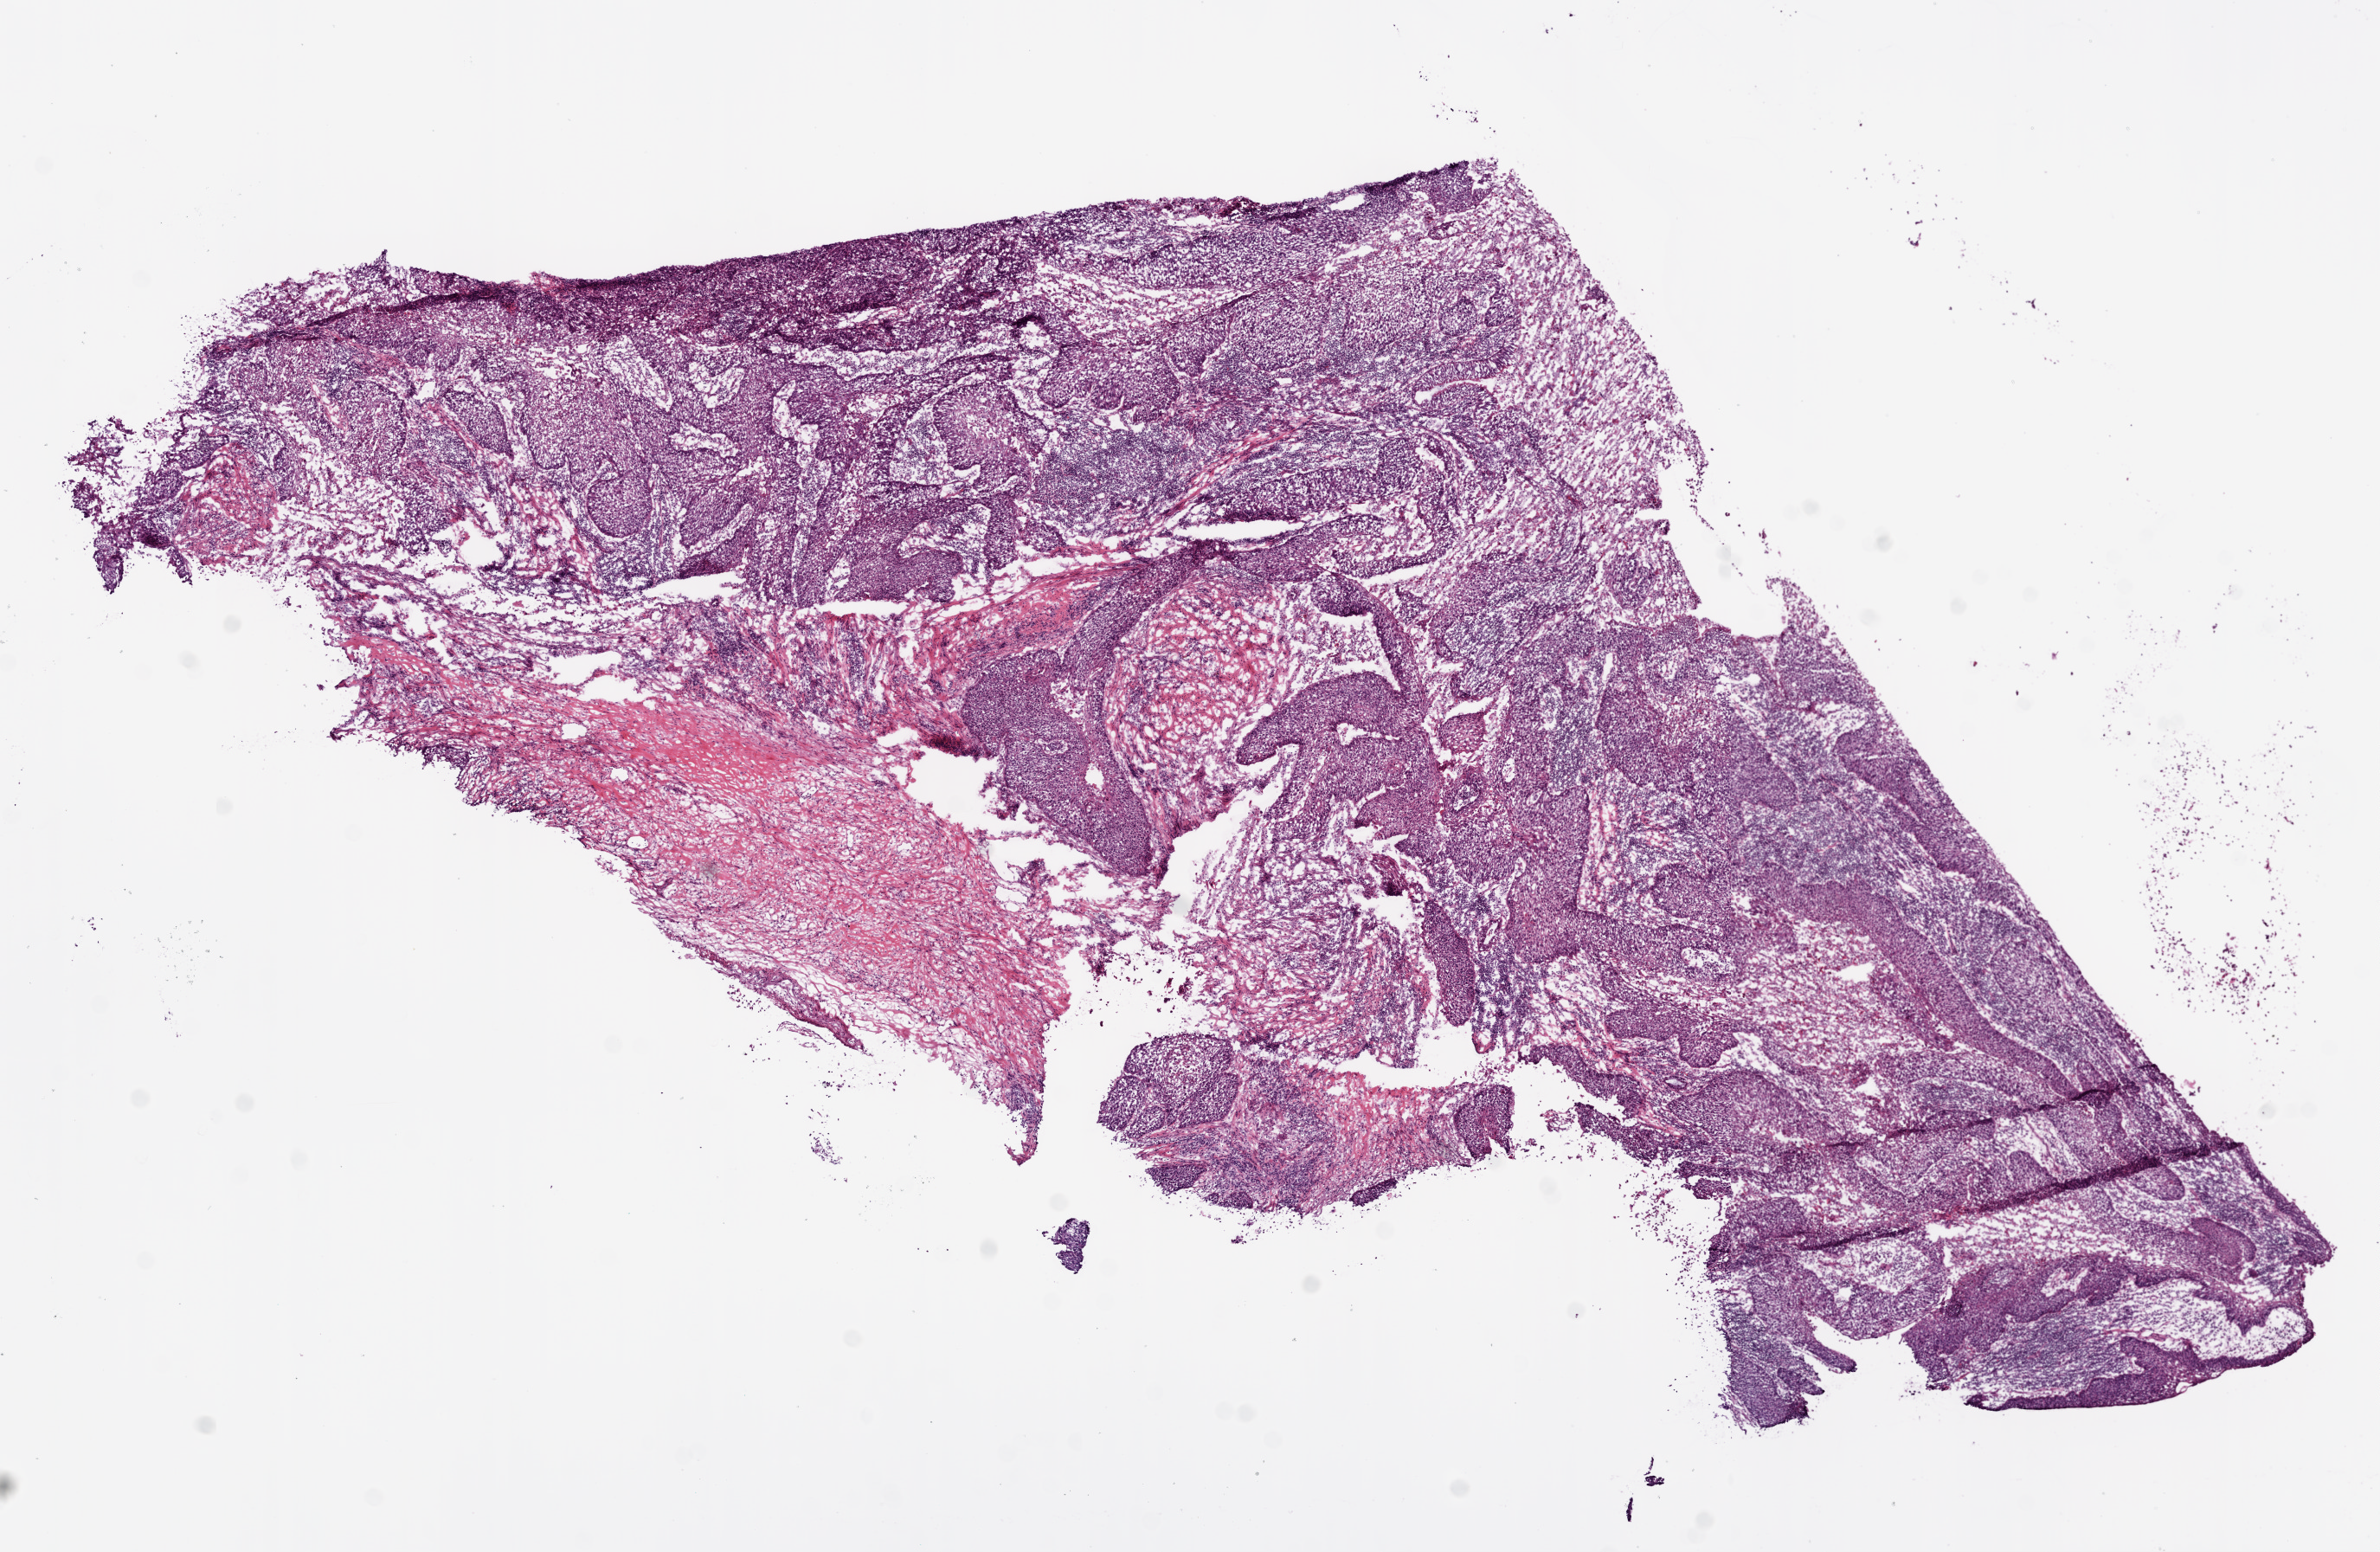
Digitized H&E tissue section (whole slide) — shown as a low-resolution overview of the whole scanned area (about 11.0 x 7.2 mm, slide scanned at 20x), frozen section from the bottom of the tissue portion, head and neck, primary tumour sample. Patient: male, age at initial diagnosis 71 years. Histologic grade: G2 (moderately differentiated). Pathologist review of this section (percent, as recorded): tumour cells 85%, tumour nuclei 59%, normal cells 0%, stromal cells 13%, necrosis 2%. Infiltration values recorded for this section: lymphocyte infiltration 36%, neutrophil infiltration 2%.
AJCC pathologic stage: IVA (6th edition). Histologic diagnosis: Squamous cell carcinoma, NOS.